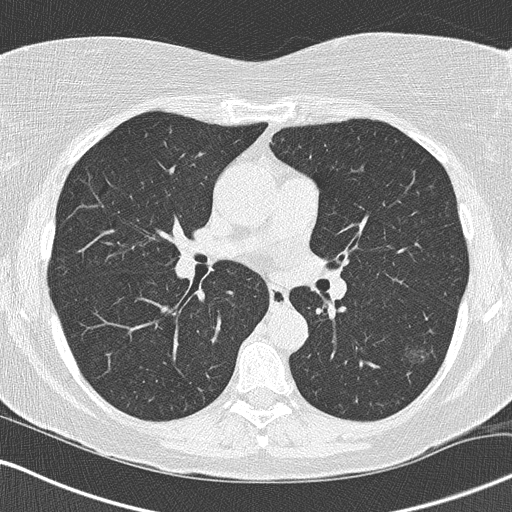
Chest CT (low-dose screening protocol), one axial image. Third annual screen. Lung window (W 1500 / L -600 HU). 2 mm slice thickness. Female, age 57 years at enrolment.
Expert-annotated lung lesion, bounding box [x1, y1, x2, y2] px = [389, 326, 456, 380]. The screening reader recorded 5 non-calcified nodules or masses ≥4 mm on this exam (left lower lobe, right upper lobe, right lower lobe, right upper lobe); which of them this box marks is not recorded. Later outcome: lung cancer diagnosed 51 days after this screen — bronchiolo-alveolar adenocarcinoma, NOS, left lower lobe, well differentiated (G1), stage IA (AJCC 6th edition), 16 mm at pathology.